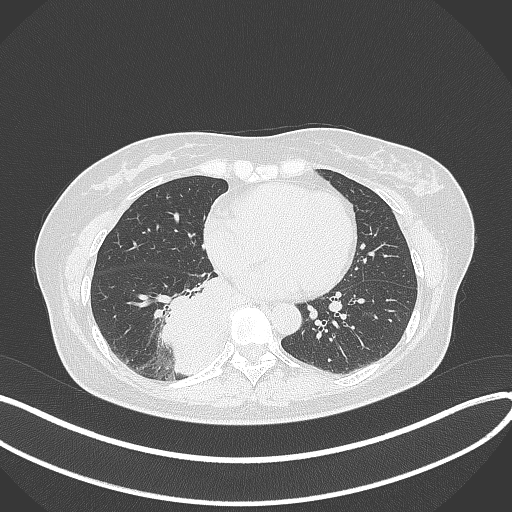
Chest CT, one axial slice. Position 138 of 331 along the scan axis. Lung window (W 1500 / L -600 HU). 1 mm slice thickness. 512 × 512 image matrix, field of view 400 × 400 mm. Patient: female, 54 years. Case-level facts recorded for this patient, not image findings: clinical TNM (as recorded): T4 N0 M0.
Annotated regions visible in this slice (rectangle marked by the reading radiologist):
- lung tumour (recorded histology: adenocarcinoma): bounding box (x1, y1, x2, y2) in pixels: (160, 271, 237, 378)